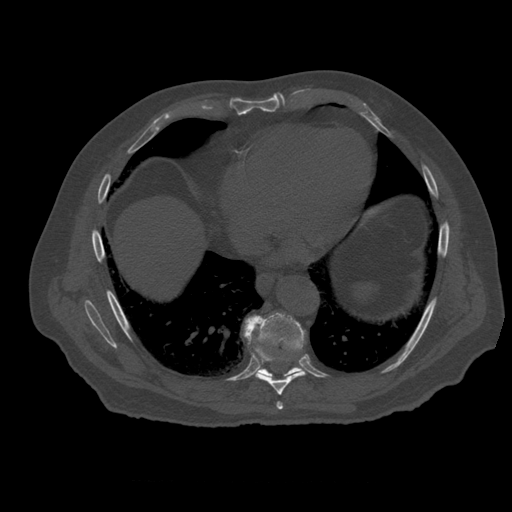
CT including the spine, one axial slice; position 333 of 399 along the scan axis; reconstruction kernel STANDARD; bone window (W 1800 / L 400 HU); 1.25 mm slice thickness; 512 × 512 image matrix, field of view 407 × 407 mm. Patient age 73 years. From the clinical record (not read from this slice): primary cancer: prostate; vertebrae with lytic lesions (as recorded): L2.
Annotated regions visible in this slice (semi-automatic segmentation, software-assisted and operator-edited):
- T7 vertebra: bounding box (x1, y1, x2, y2) in pixels: (277, 402, 284, 410)
- T8 vertebra: (256, 345, 303, 396)
- T9 vertebra: (245, 313, 306, 378)